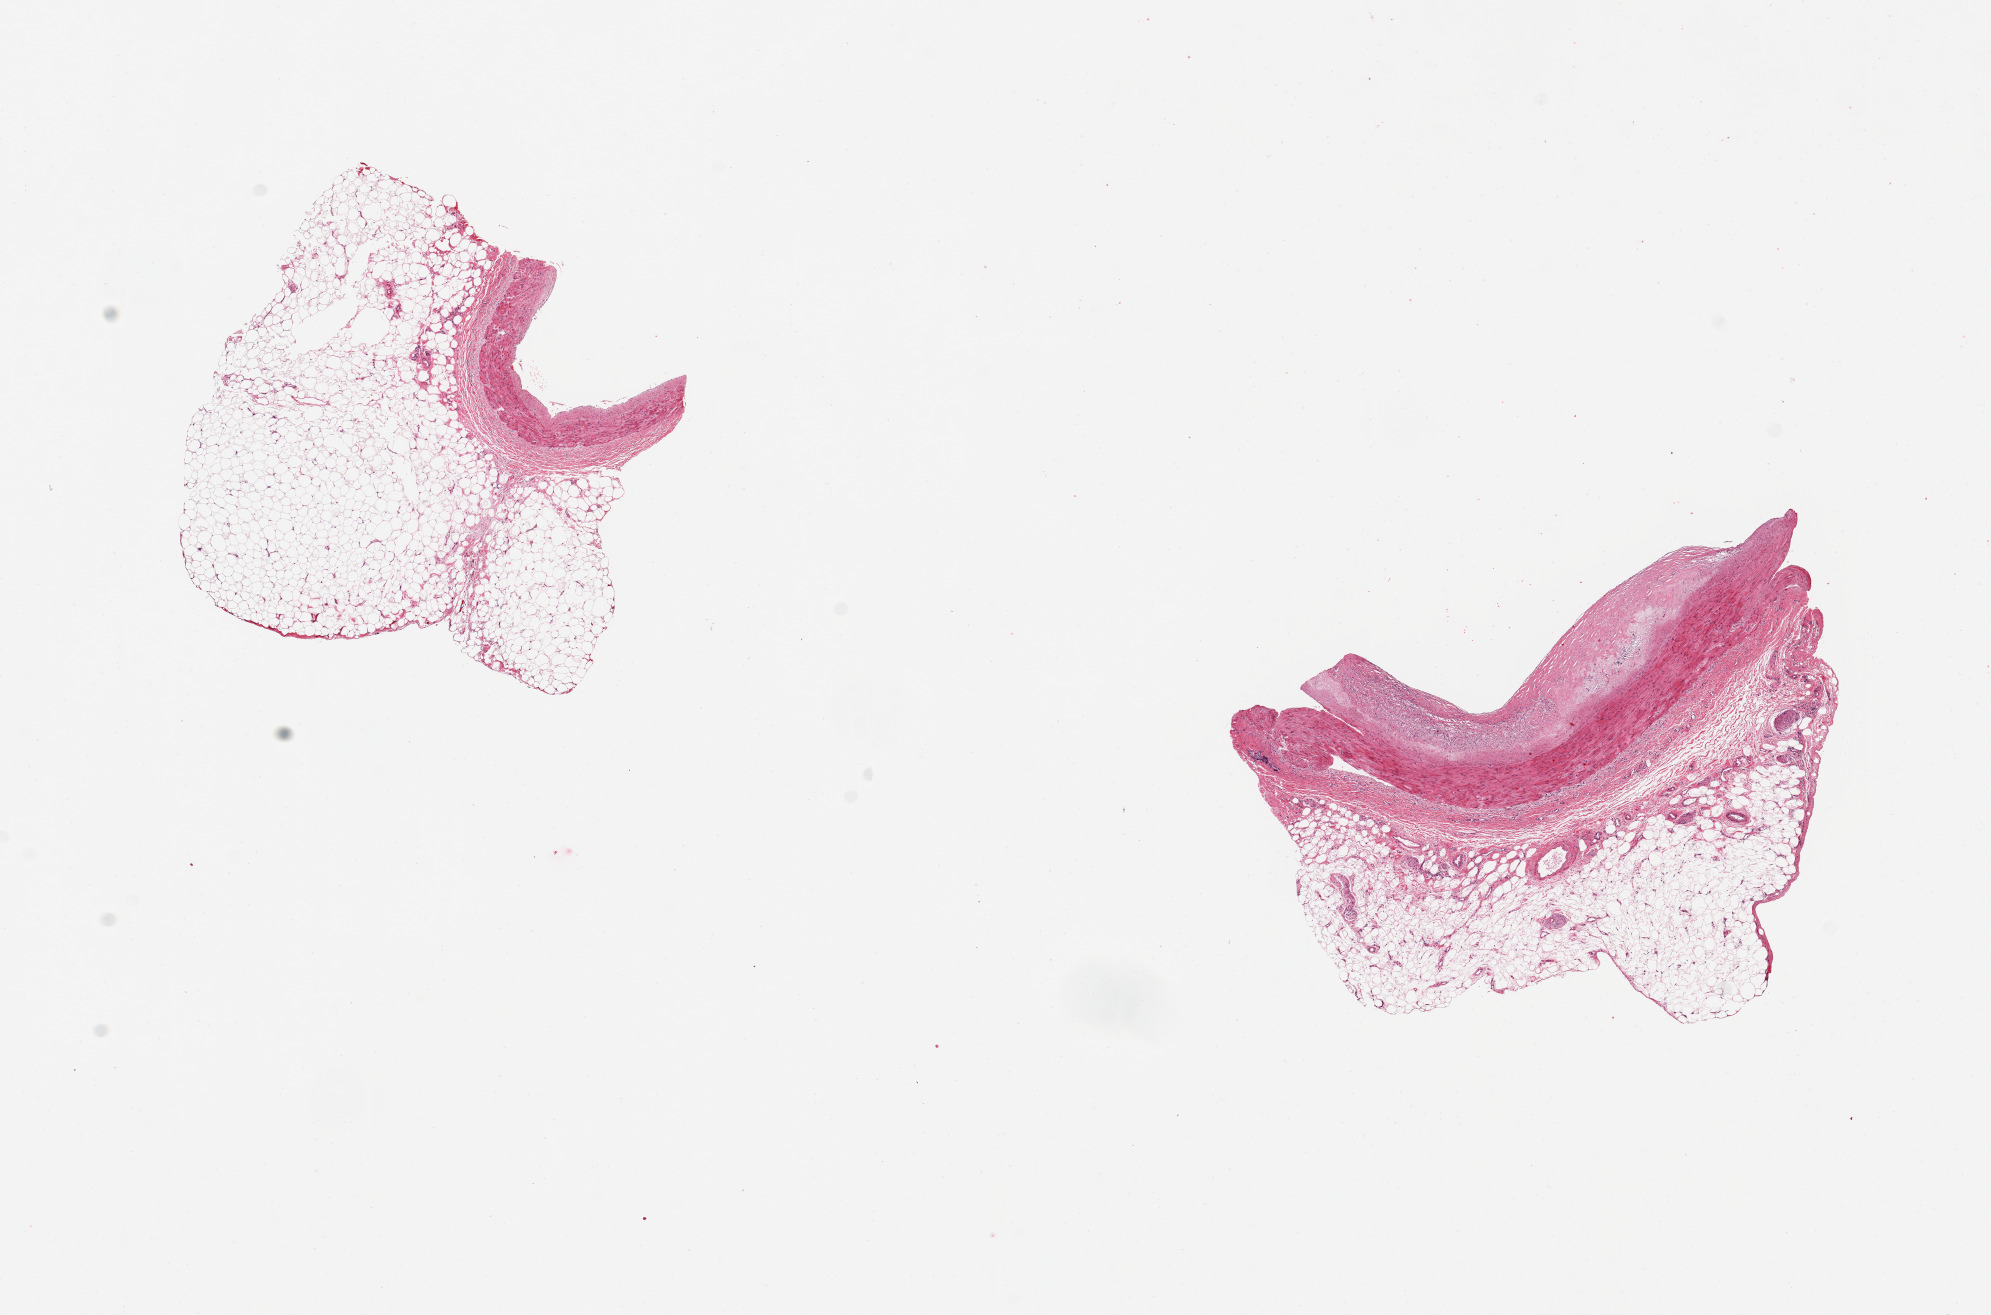
Haematoxylin and eosin whole-slide image — low-resolution overview of the scanned area, about 15.8 x 10.4 mm (from a 20x scan). PAXgene-fixed paraffin-embedded (PFPE) section. Target tissue: coronary artery. Tissue donor sample. Donor sex: male.
Review note (as recorded): 2 pieces, hemisections, adherent nubbins of fat up to ~2mm; ~50% occlusive atherosis noted in one section (est).